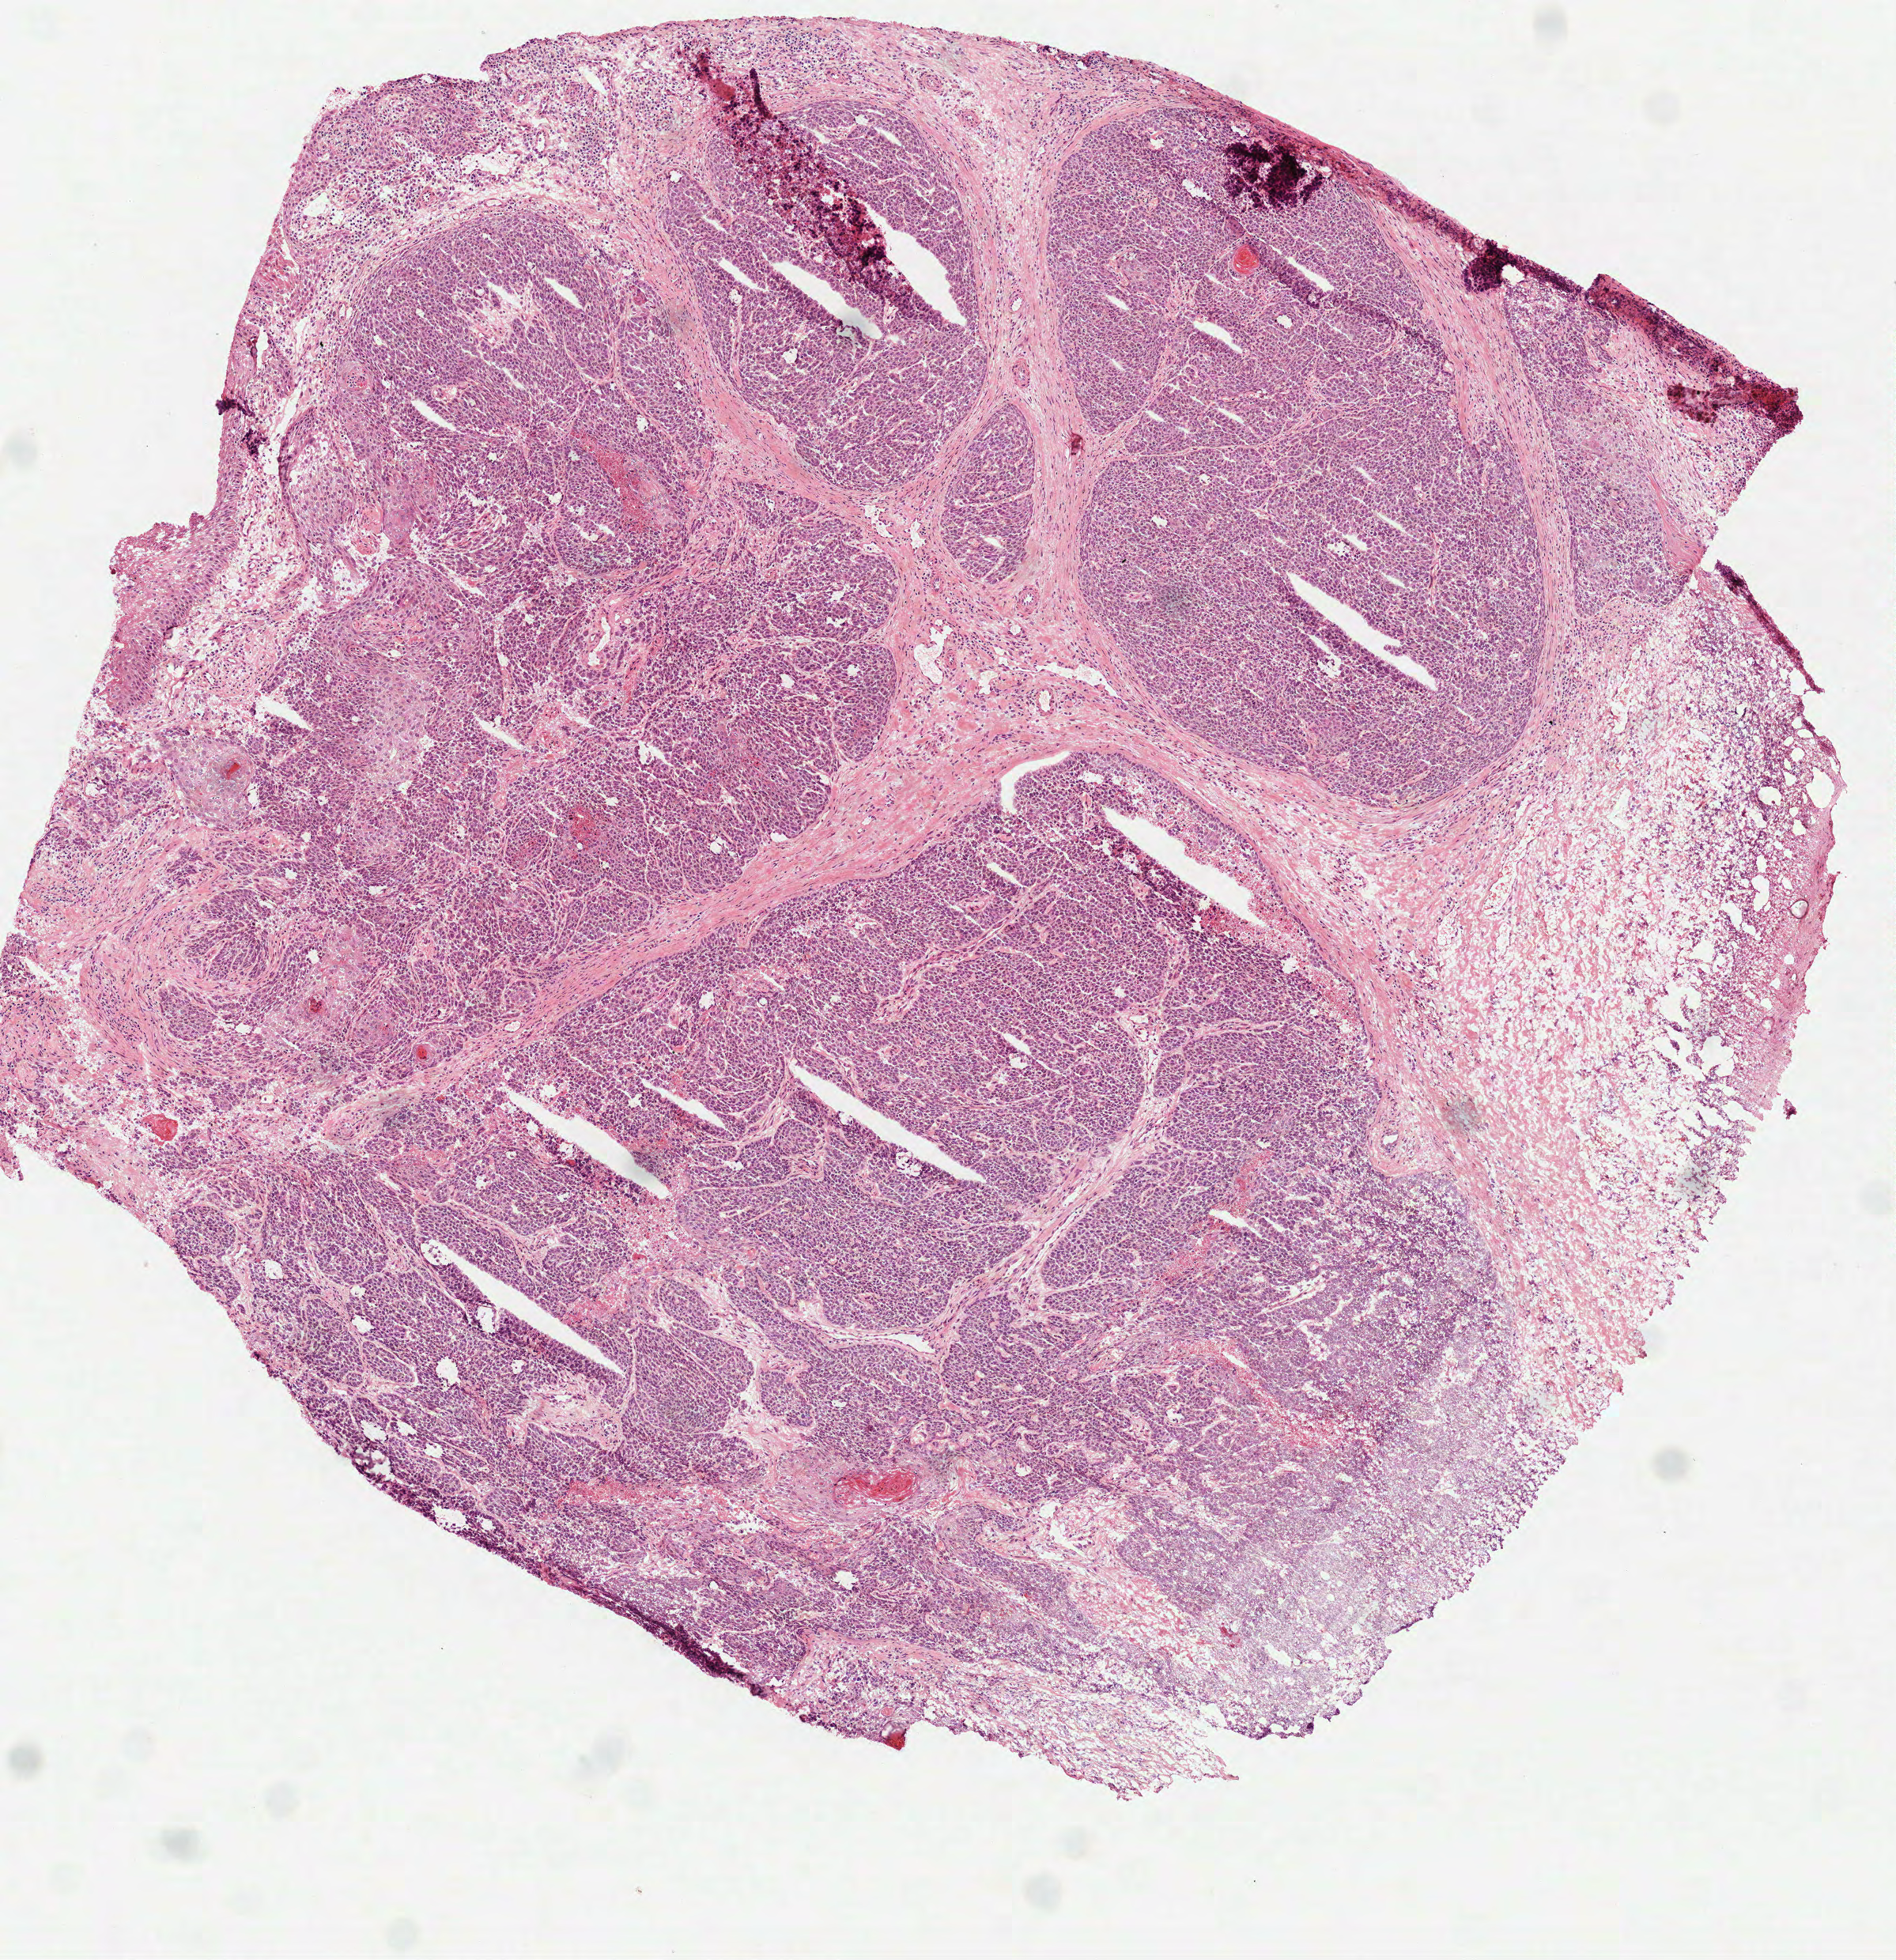
Digitized H&E tissue section (whole slide), shown as a low-resolution overview of the whole scanned area (about 4.8 x 5.0 mm, acquisition: 40x scan), frozen section from the top of the tissue portion, head and neck, primary tumour sample. Female patient; age at initial diagnosis 55 years. Histologic grade: G3 (poorly differentiated). Slide review estimates, as recorded: tumour cells 75%, tumour nuclei 80%, normal cells 2%, stromal cells 20%, necrosis 3%.
TNM: T1 N0. AJCC pathologic stage: I (7th edition). Histologic diagnosis: Squamous cell carcinoma, NOS (lip, NOS).